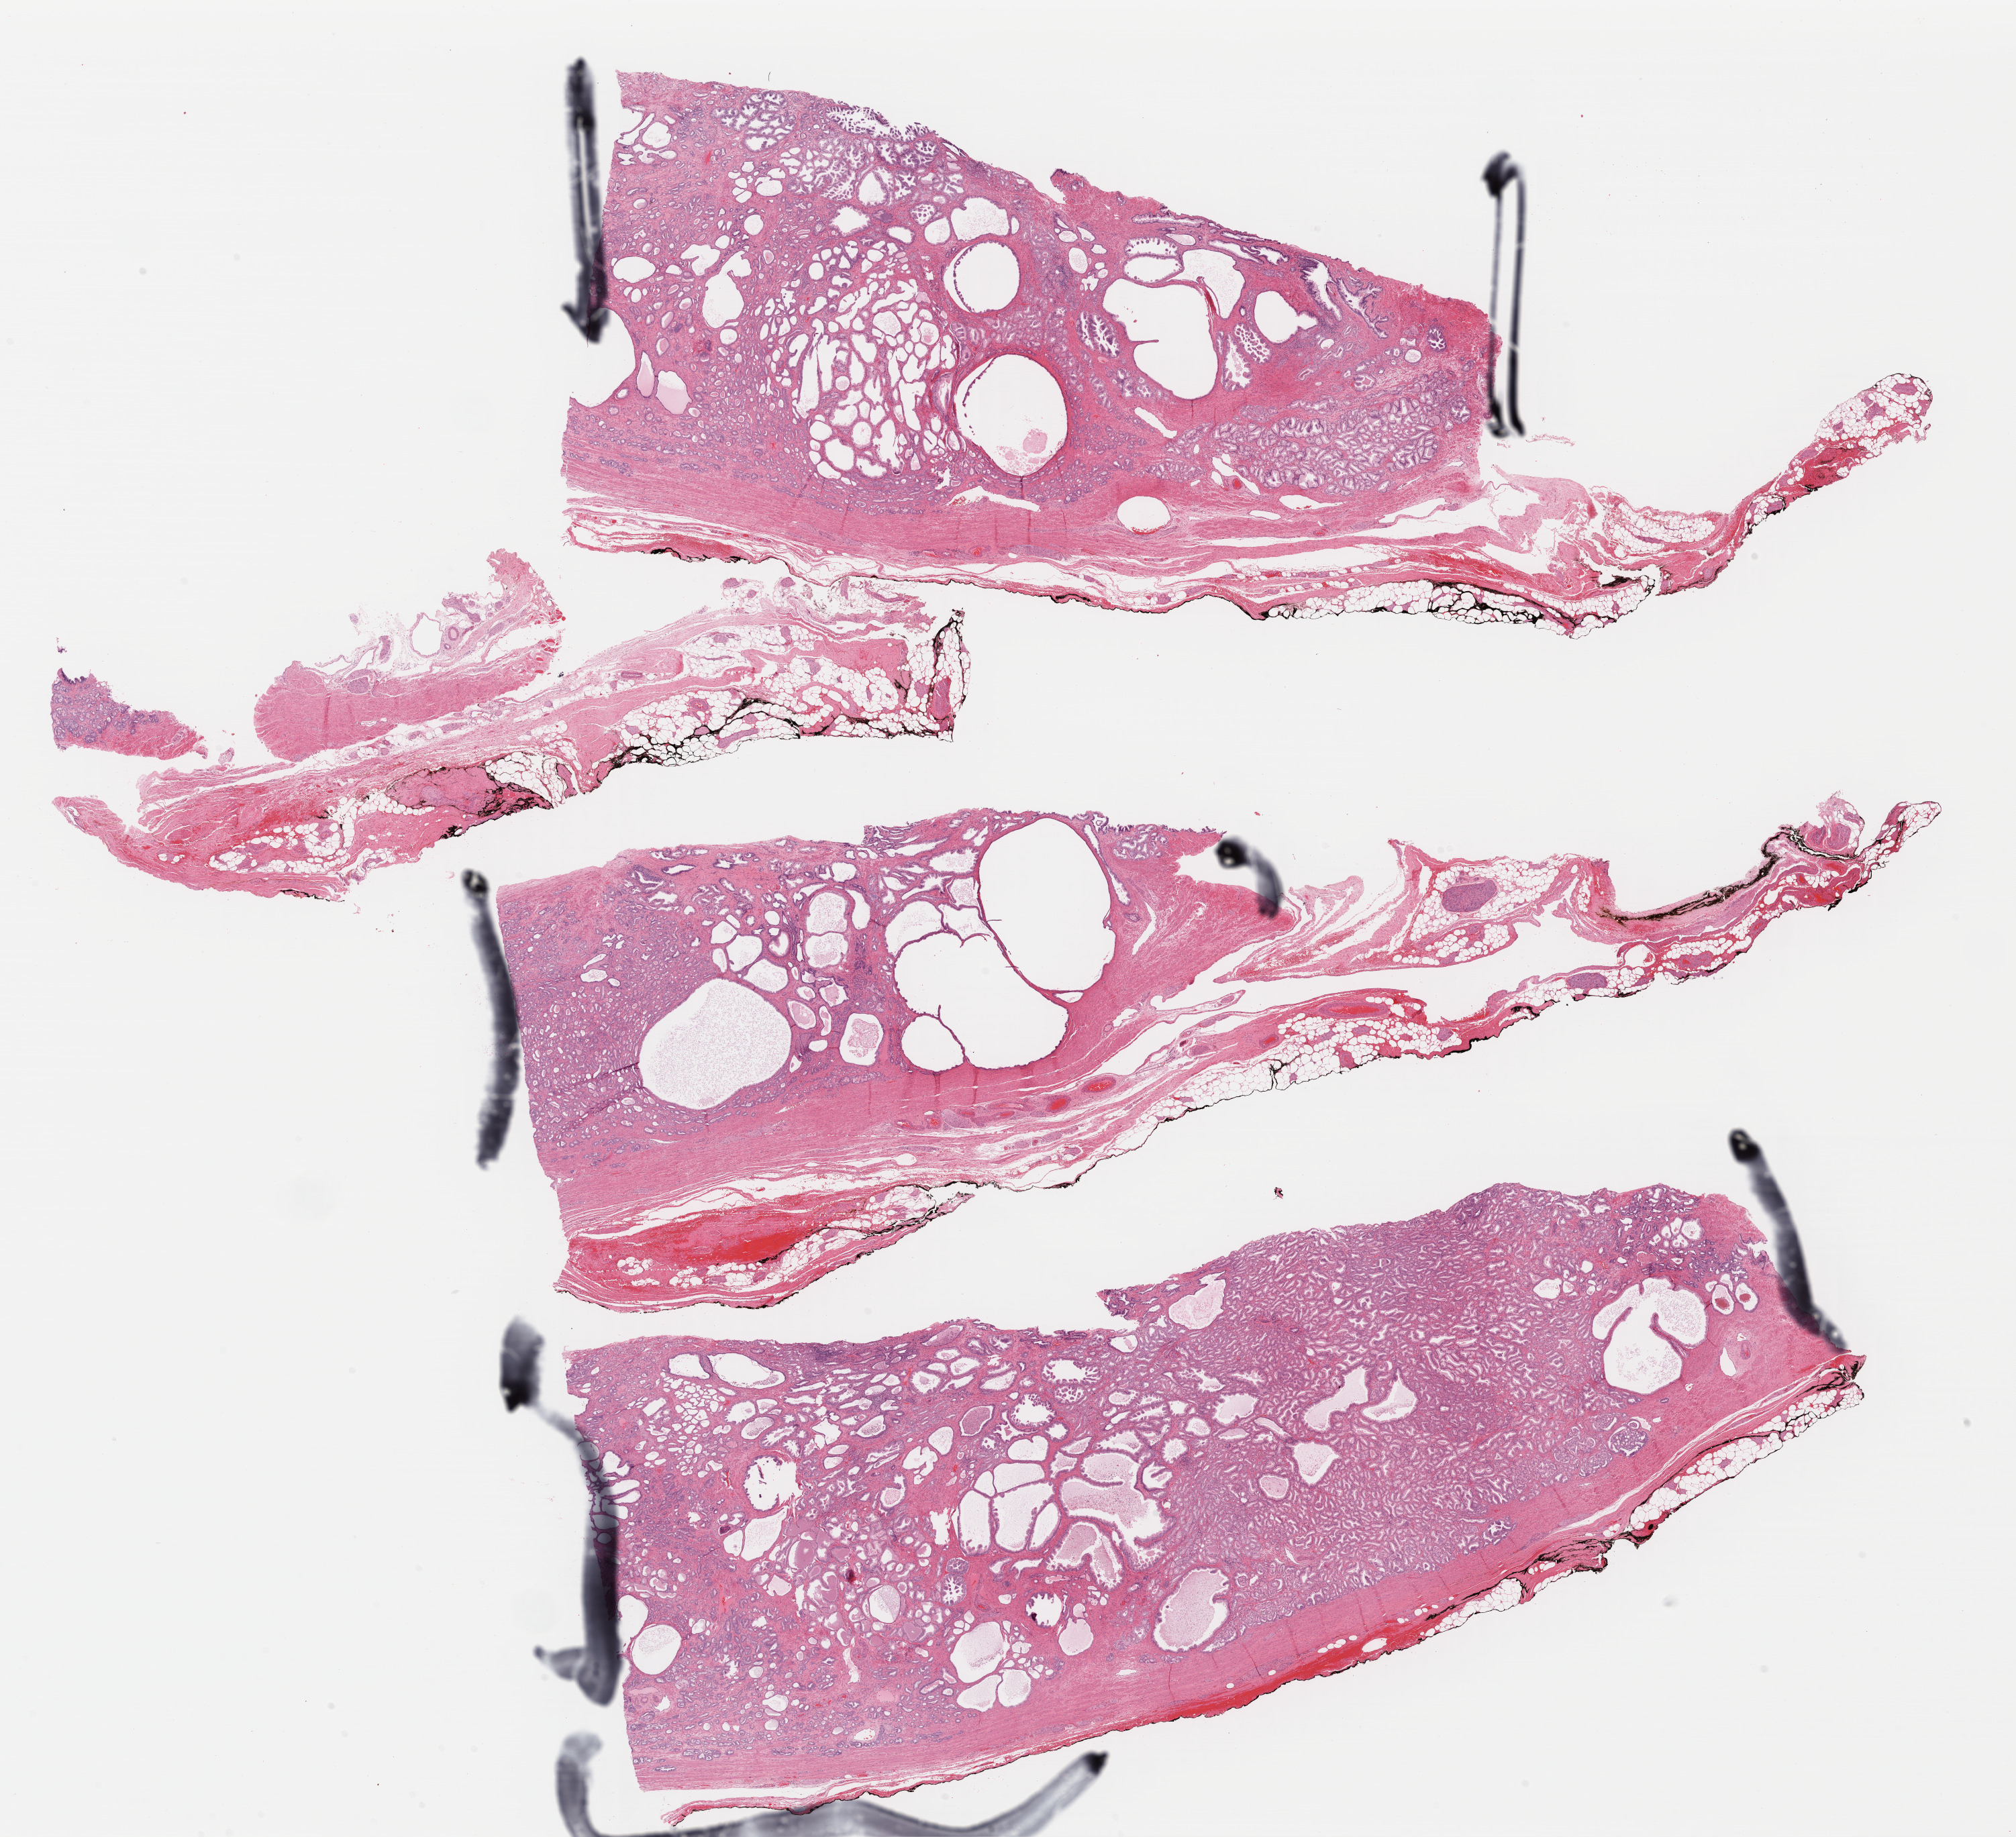
Hematoxylin and eosin (H&E) stained whole-slide image — whole scanned area (about 23.6 x 21.5 mm) shown as a low-resolution overview. Formalin-fixed paraffin-embedded (FFPE) diagnostic section. Prostate, primary tumour sample. Male, age 57 years at initial diagnosis. Gleason score: 7 (3+4).
Histologic diagnosis: Adenocarcinoma, NOS (prostate gland).